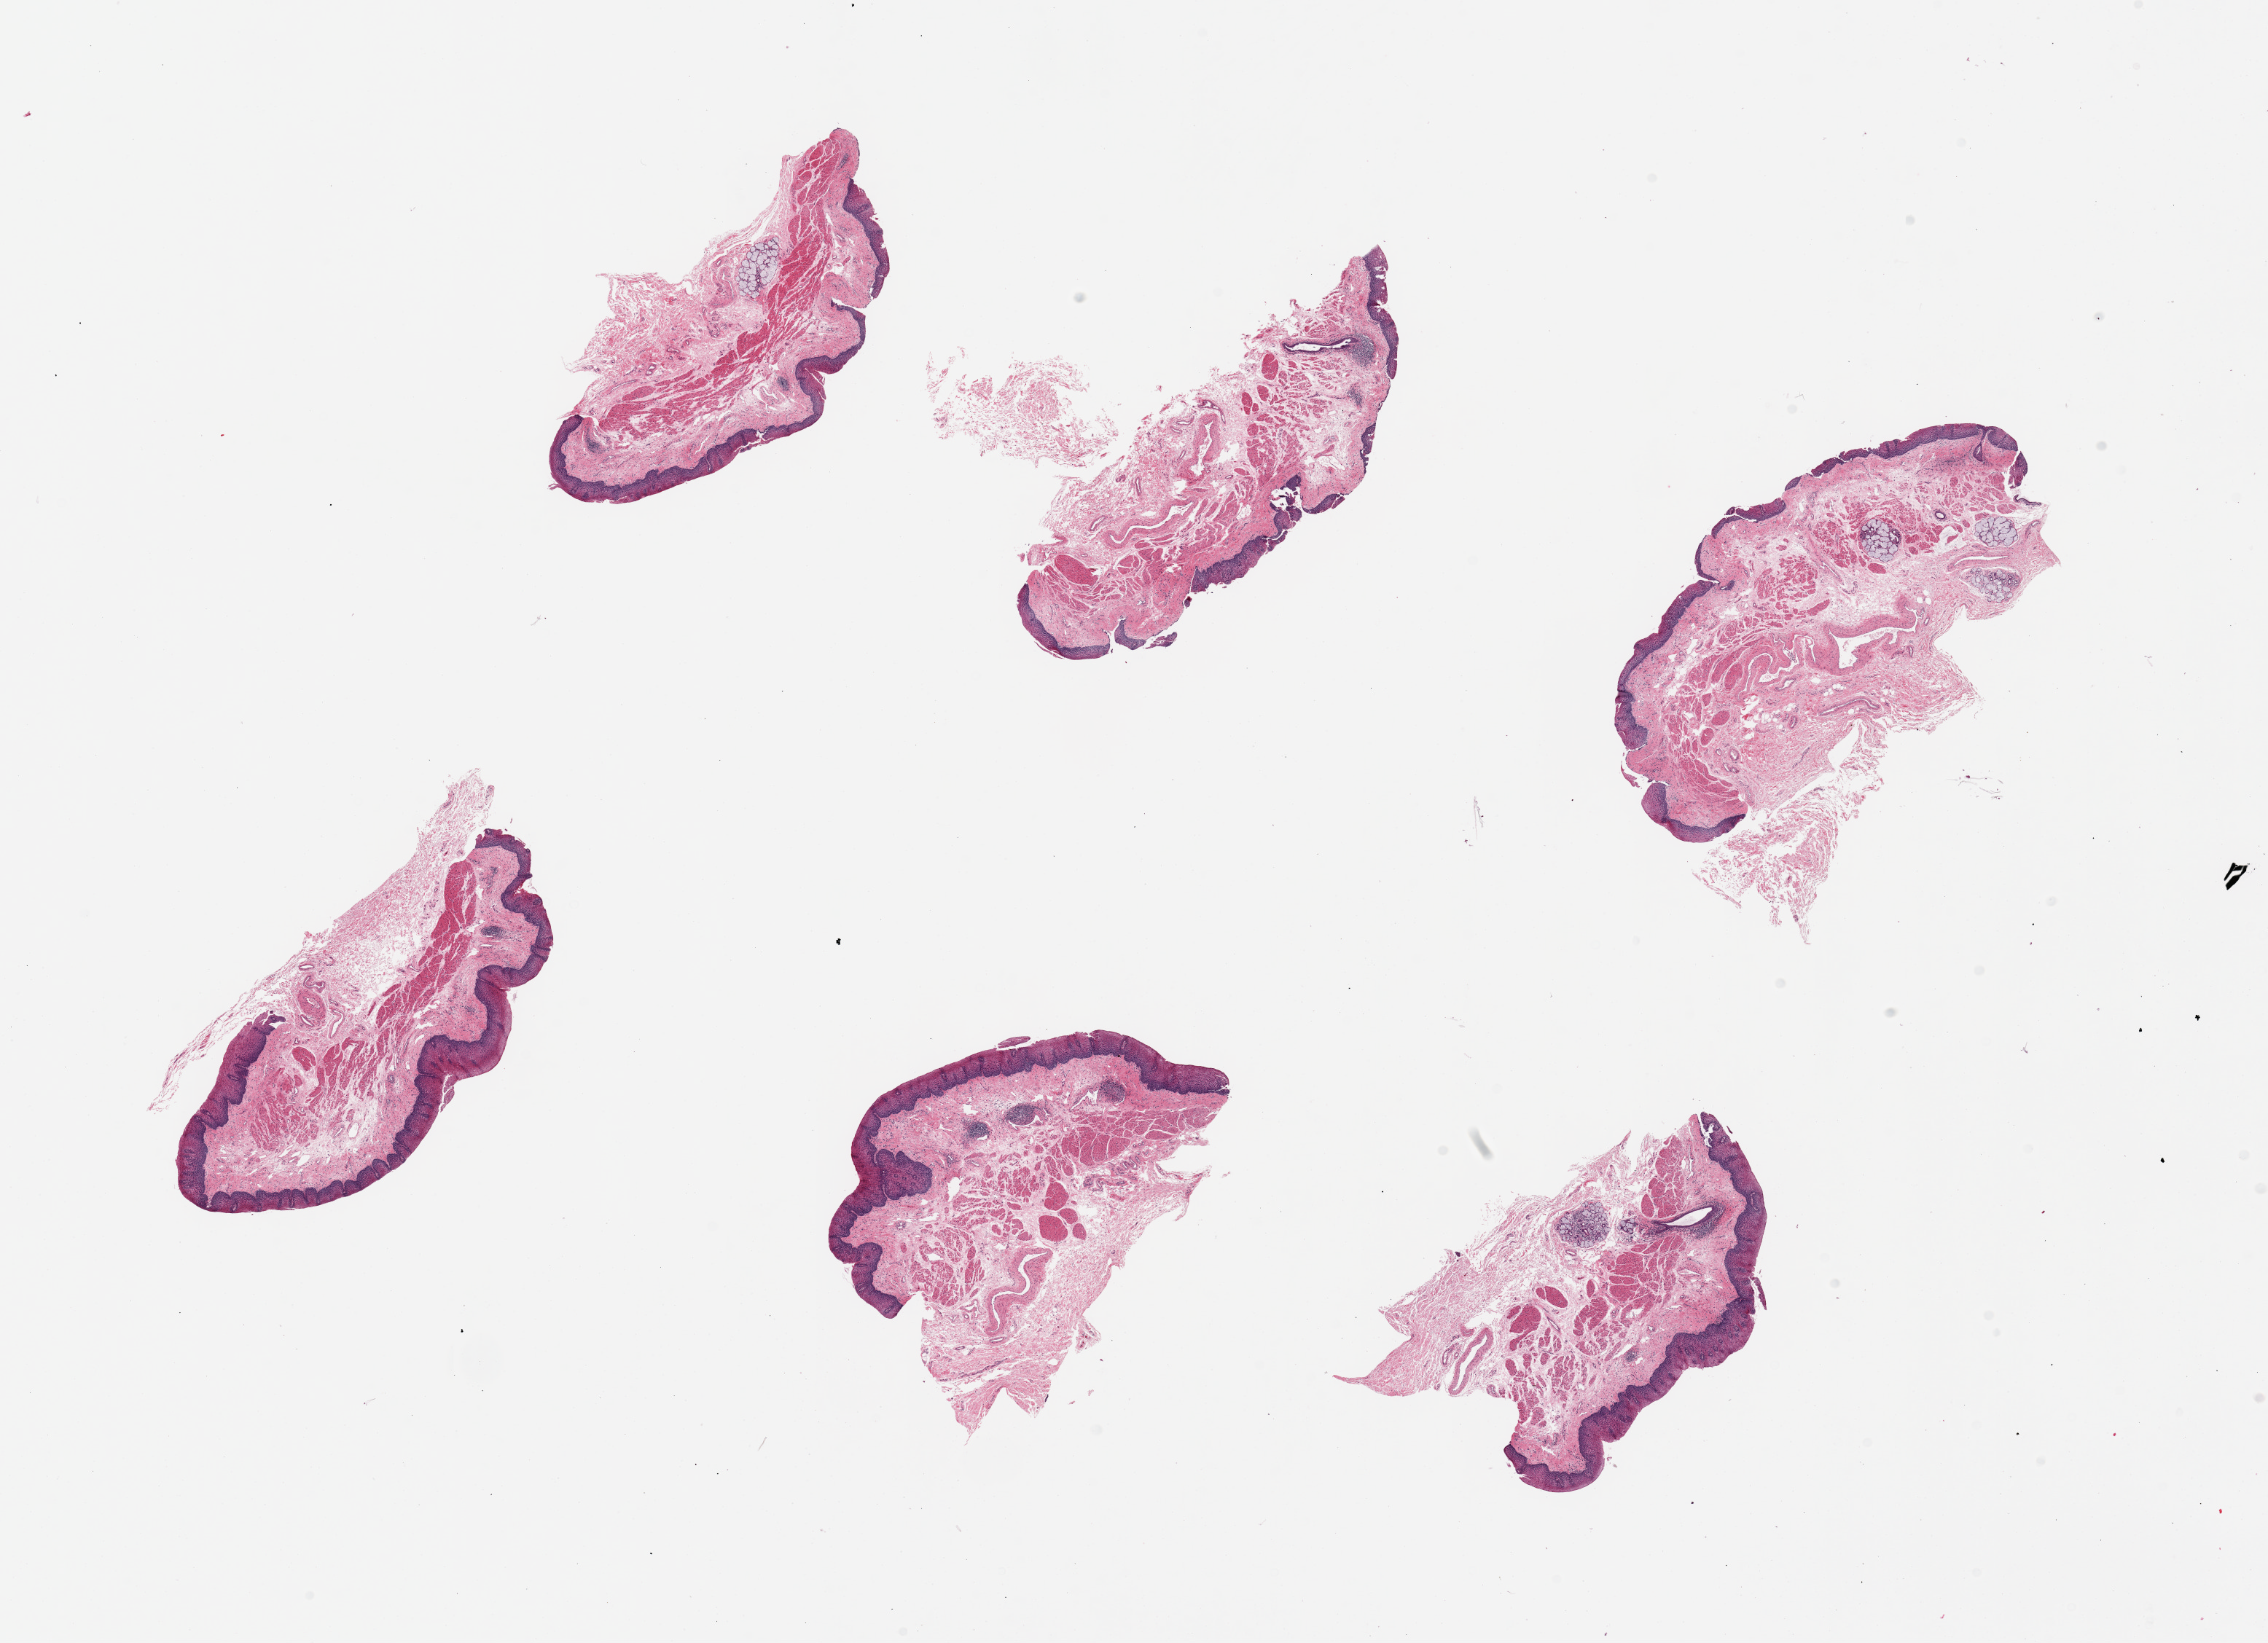
Whole-slide image, H&E stain — whole scanned area (about 24.6 x 17.8 mm) shown as a low-resolution overview. PAXgene-fixed, paraffin-embedded tissue. Sampled site (target tissue): esophageal mucous membrane. Tissue donor sample. Donor sex: male.
Review note (as recorded): 6 pieces.